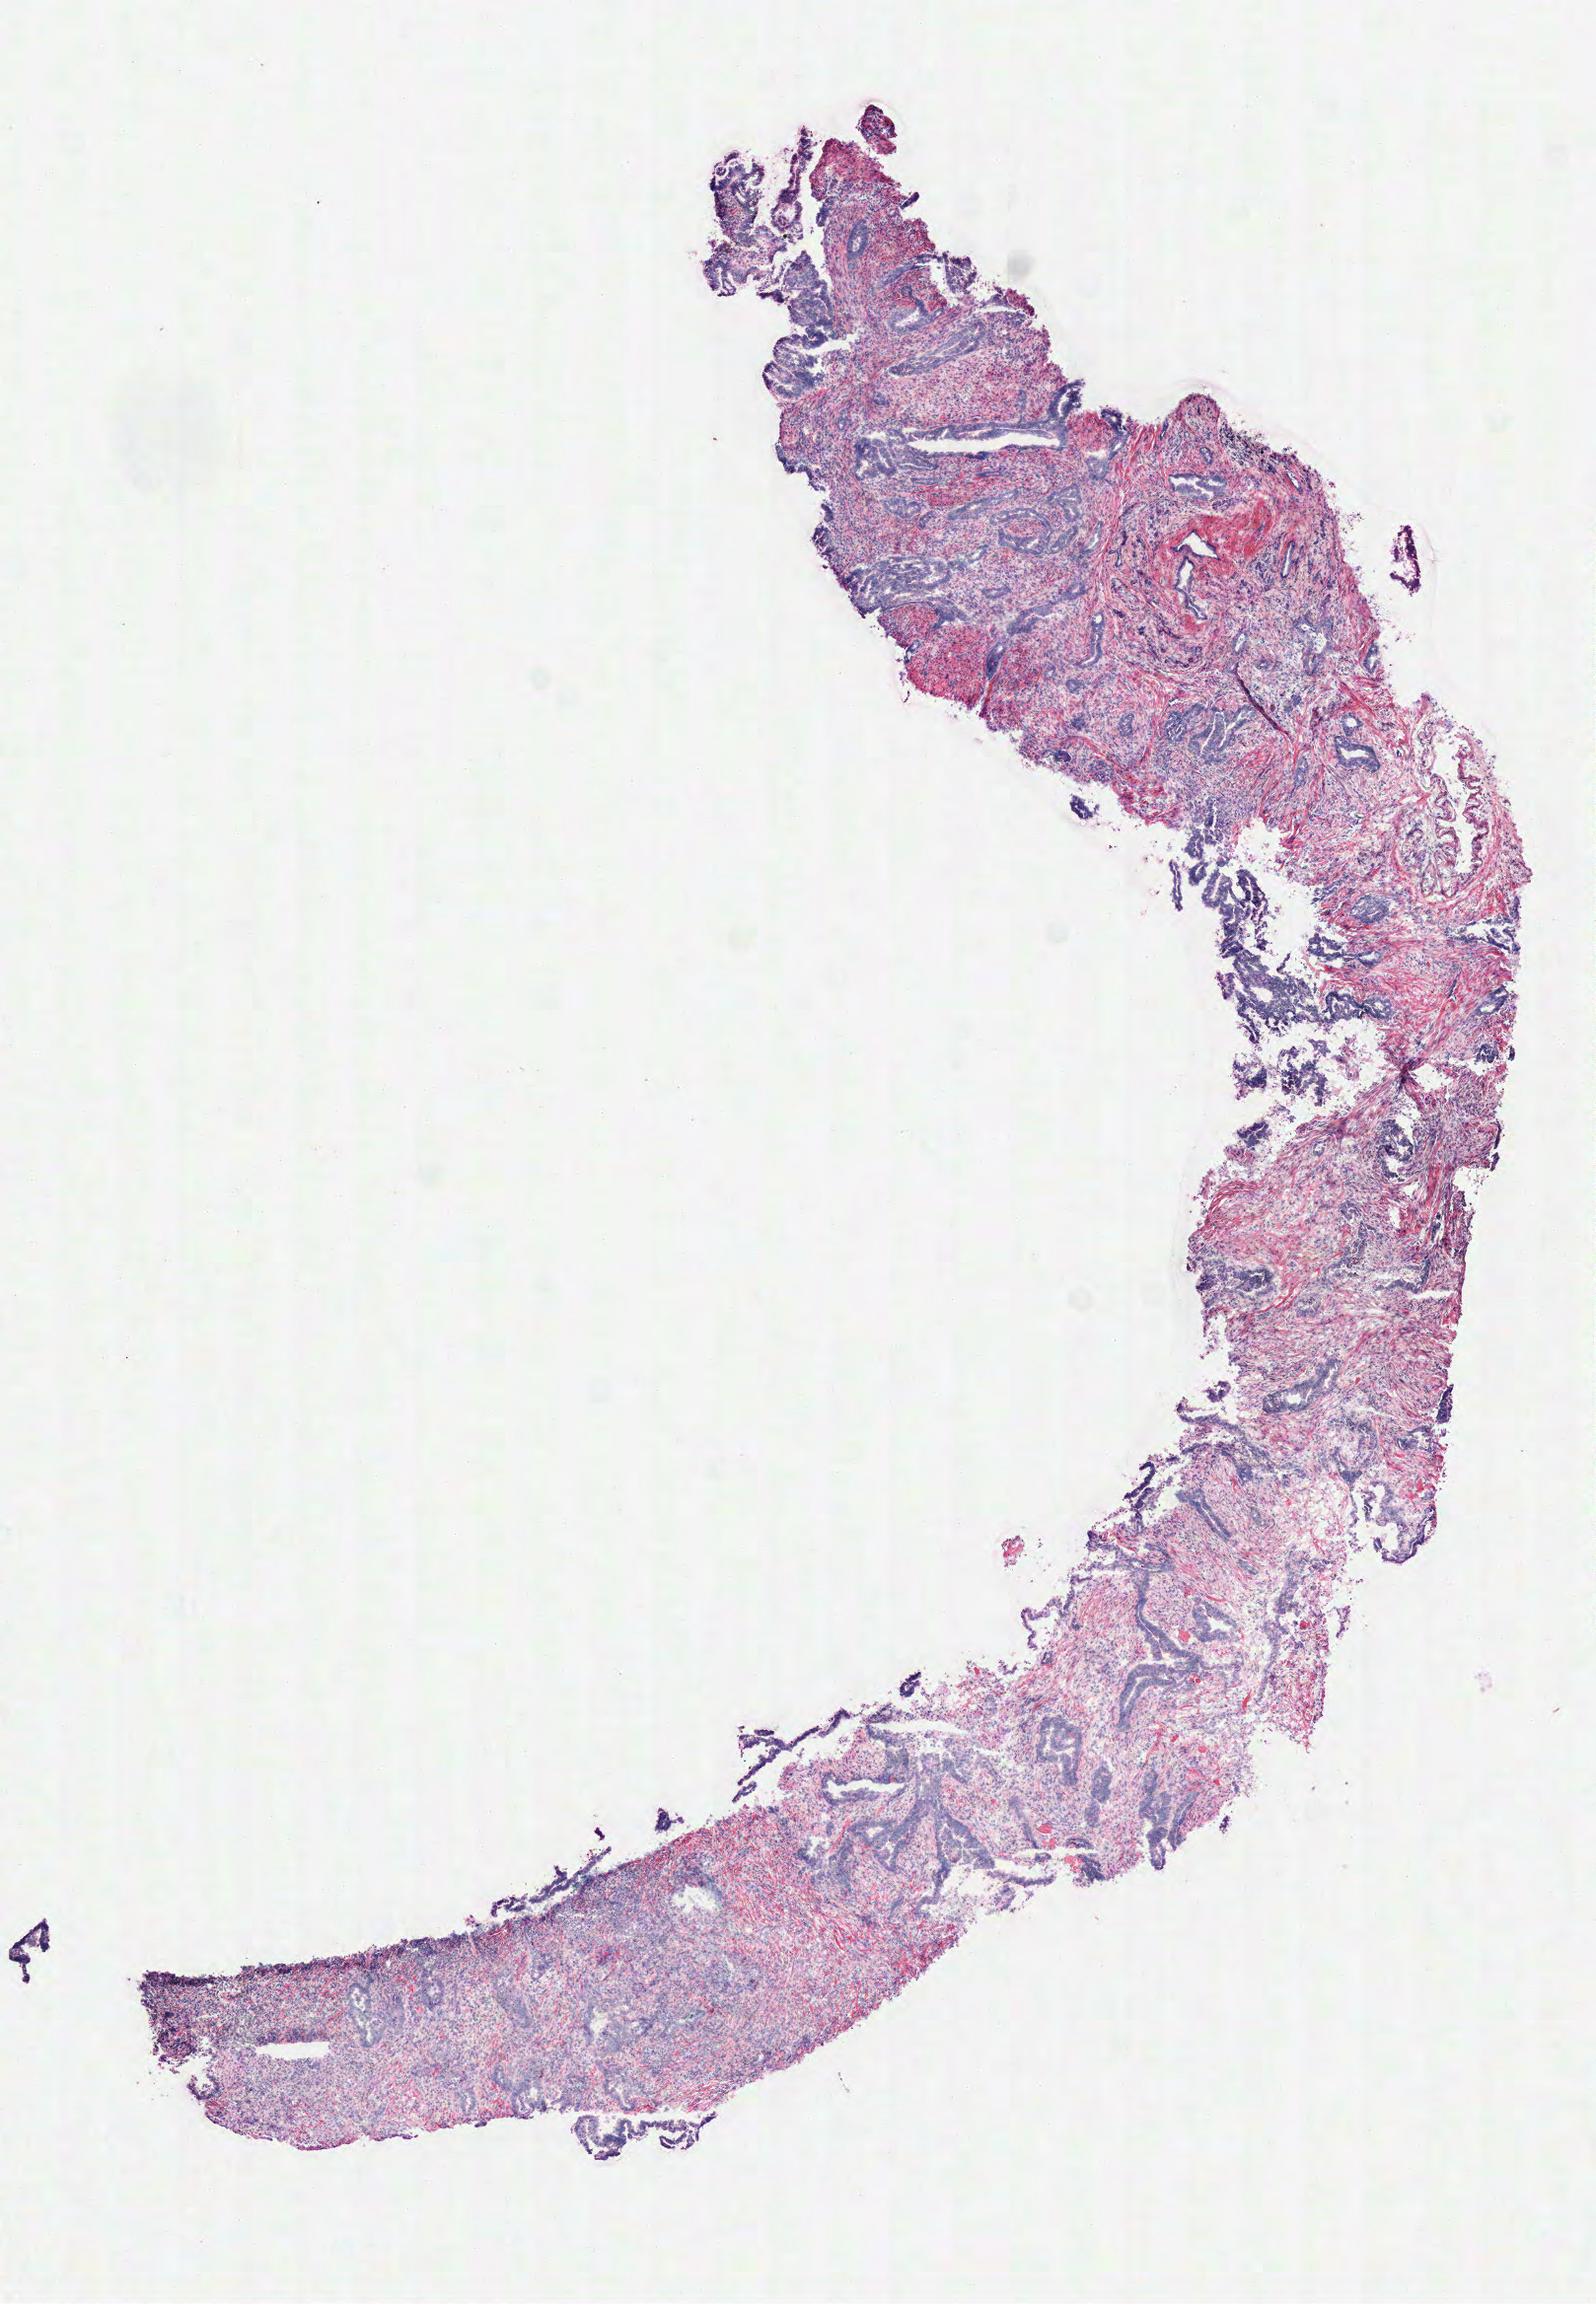
H&E whole-slide image, whole scanned area (about 6.5 x 9.4 mm) shown as a low-resolution overview. Frozen section from the top of the tissue portion. Pancreas, primary tumour sample. Female patient; age at initial diagnosis 65 years. Histologic grade: G2 (moderately differentiated). Slide review estimates, as recorded: tumour cells 100%, tumour nuclei 50%, normal cells 0%, stromal cells 0%, necrosis 0%. Infiltration values recorded for this section: lymphocyte infiltration 5%, monocyte infiltration 0%, neutrophil infiltration 0%.
* histologic diagnosis: Infiltrating duct carcinoma, NOS (head of pancreas)
* lymph nodes positive (case pathology): 3 of 8 examined
* AJCC pathologic stage: IV (7th edition)